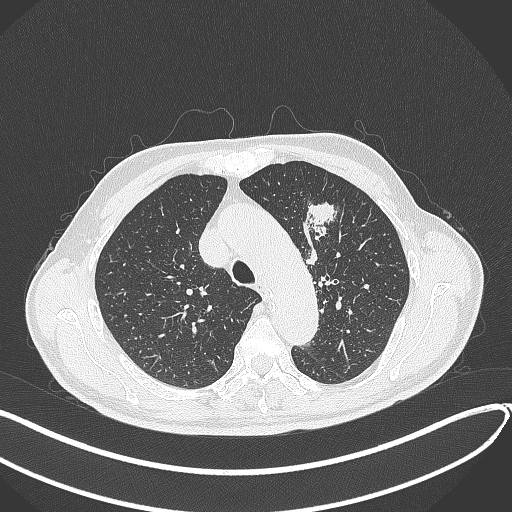
Chest CT, one axial slice. Slice 309 of 459 in the series (ordered by position). 120 kVp. Lung window (W 1500 / L -600 HU). 512 × 512 image matrix, field of view 400 × 400 mm. Male patient, age 74 years. From the clinical record (not read from this slice): clinical TNM (as recorded): T2b N0 M1c.
Annotated regions visible in this slice (rectangle marked by the reading radiologist):
- lung tumour (recorded histology: adenocarcinoma): box from (x=306, y=202) to (x=338, y=244) px